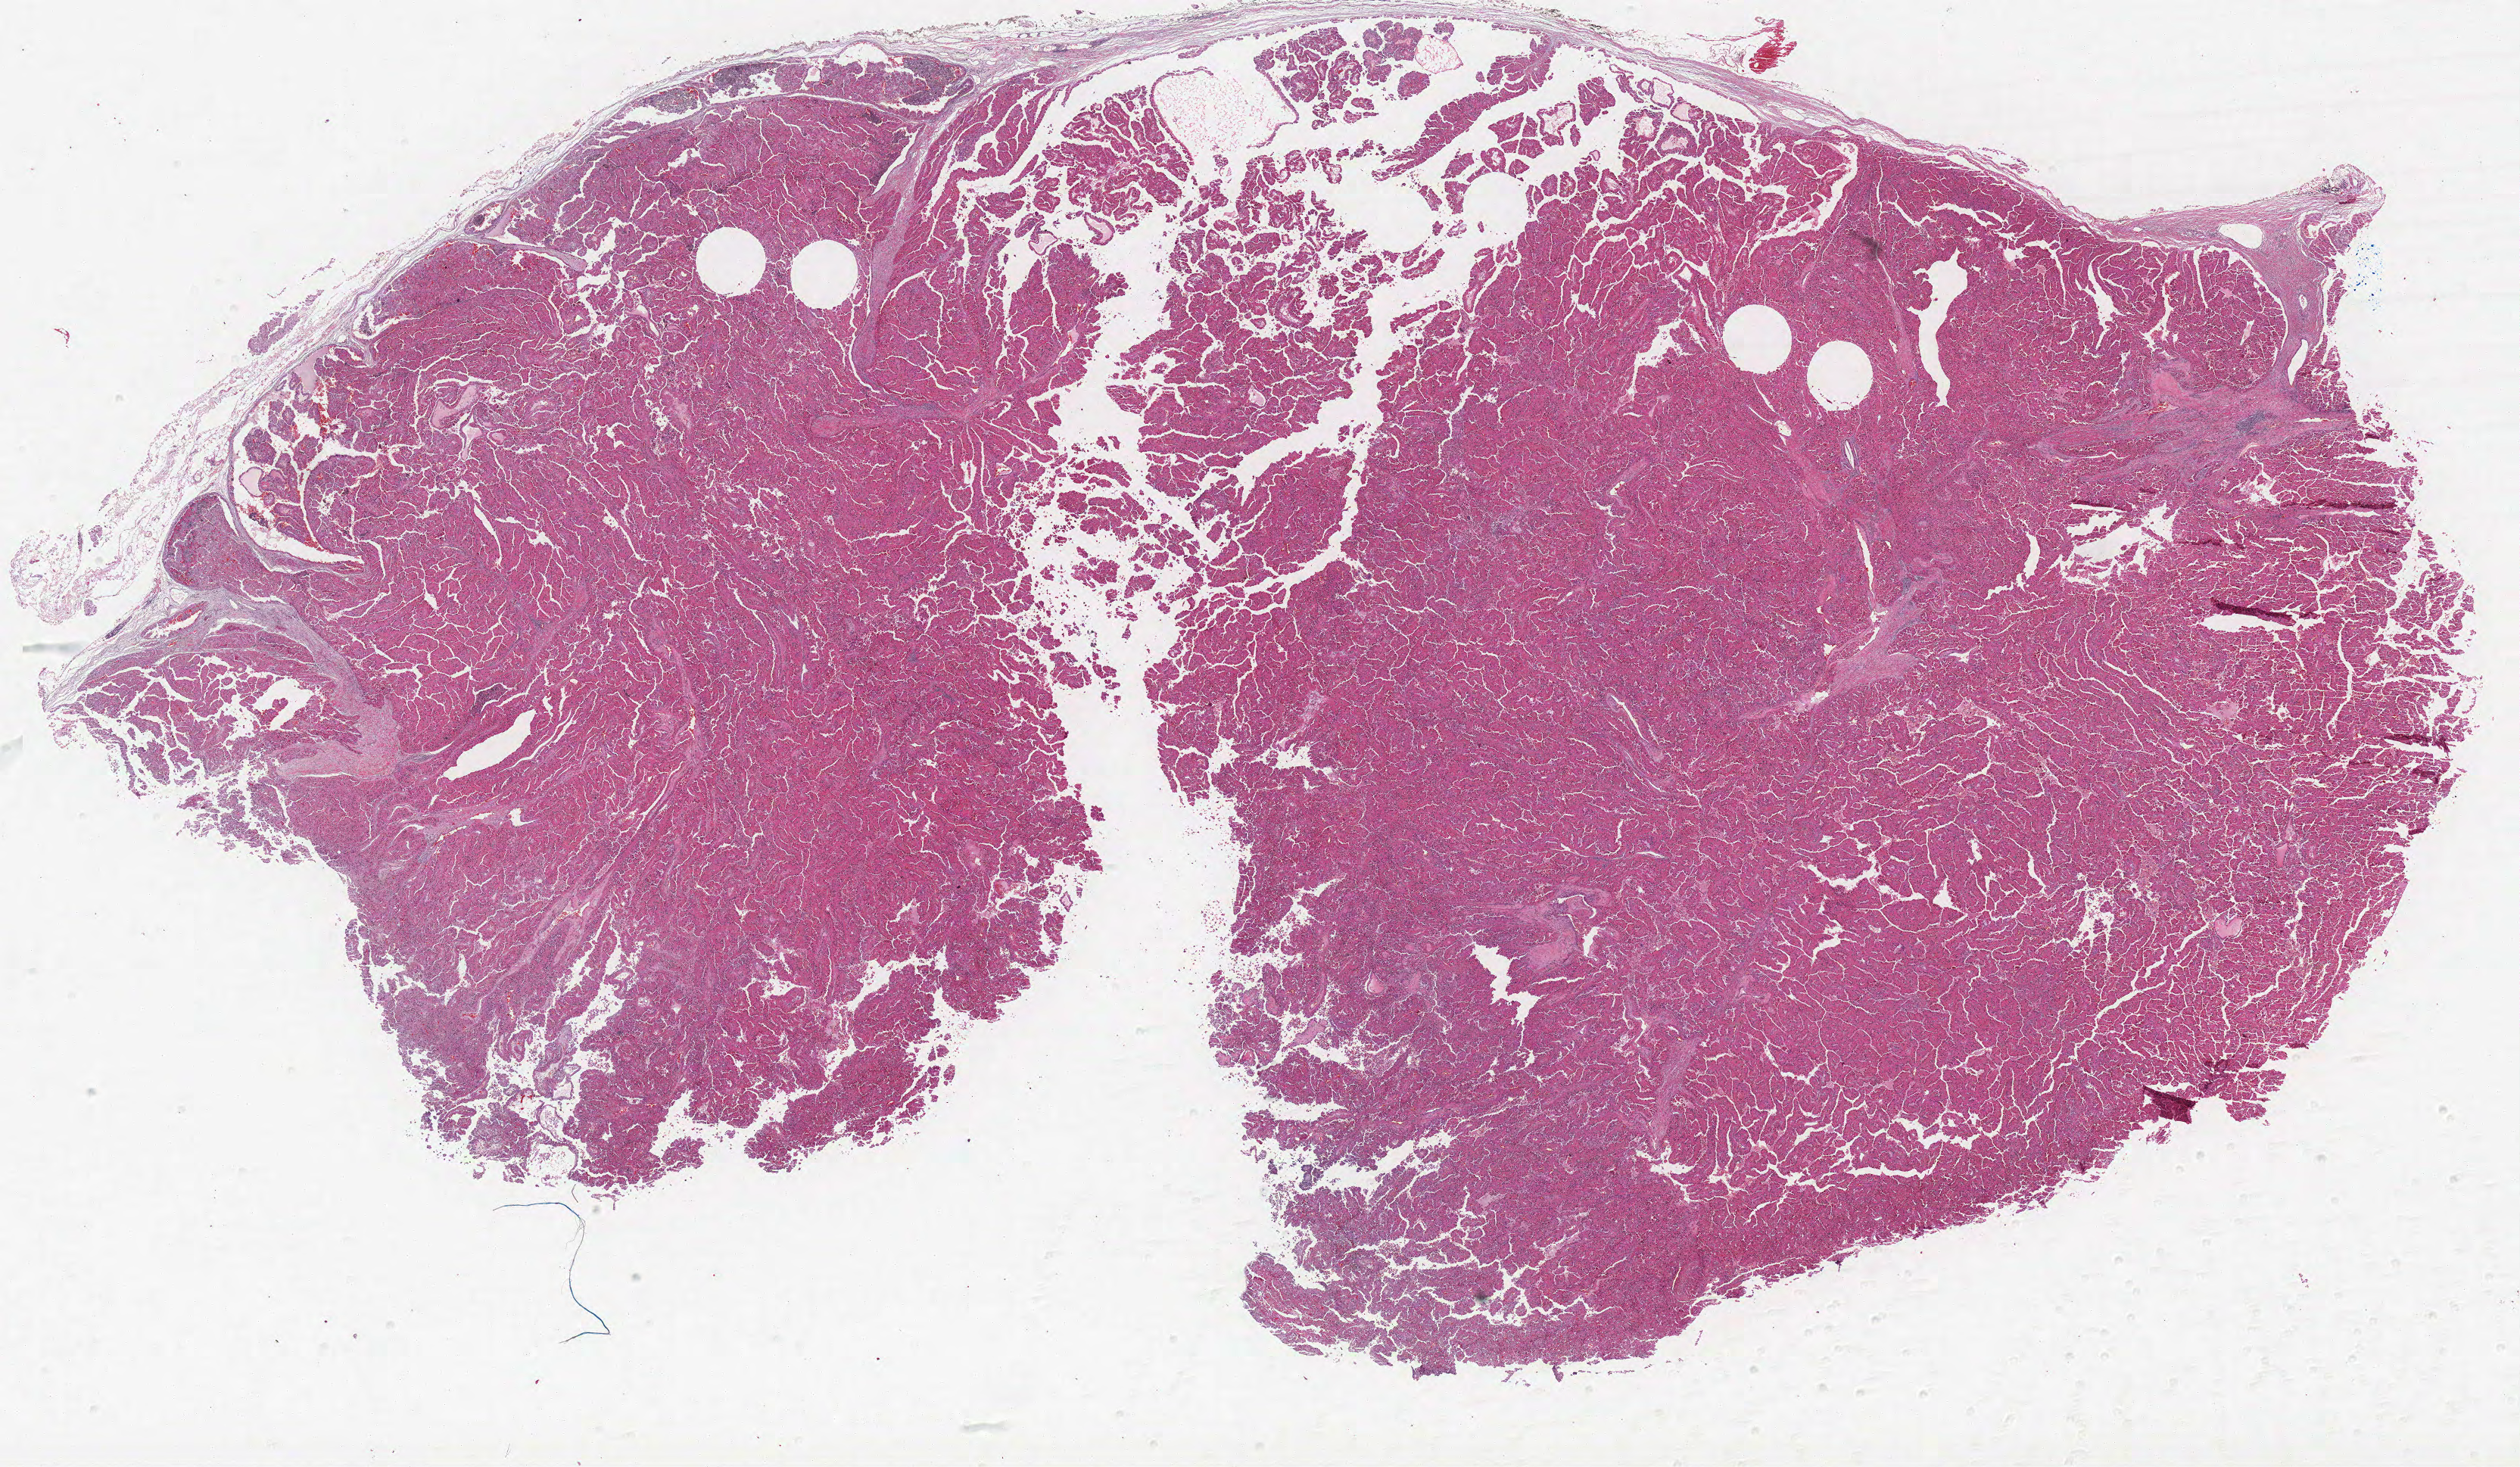
Digitized Hematoxylin and eosin (H&E) stained tissue section (whole slide), low-resolution overview of the scanned area, about 26.6 x 15.5 mm (slide scanned at 40x), formalin-fixed paraffin-embedded (FFPE) diagnostic section, primary tumour sample from the kidney. Female patient; age at initial diagnosis 66 years.
• histologic diagnosis: Papillary adenocarcinoma, NOS
• TNM: T3a NX M0
• AJCC pathologic stage: III